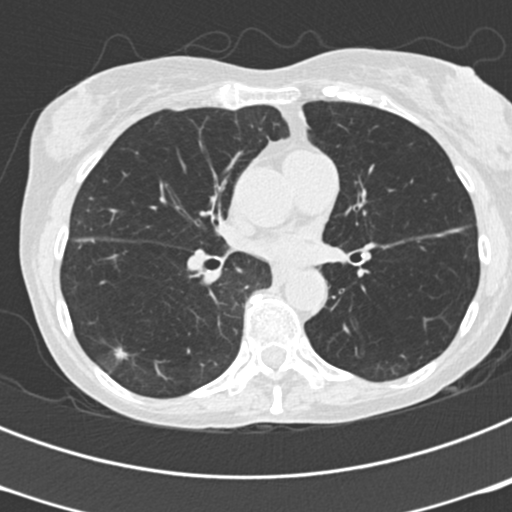
Low-dose screening chest CT, one axial slice; 120 kVp; lung window (W 1500 / L -600 HU); 2 mm slice thickness; 512 × 512 image matrix, field of view 290 × 290 mm.
Annotated regions visible in this slice (outlined manually by an expert reader):
- lesion 1 (tumor, lower lobe of right lung): bounding box [x1, y1, x2, y2] px = [114, 347, 128, 360]